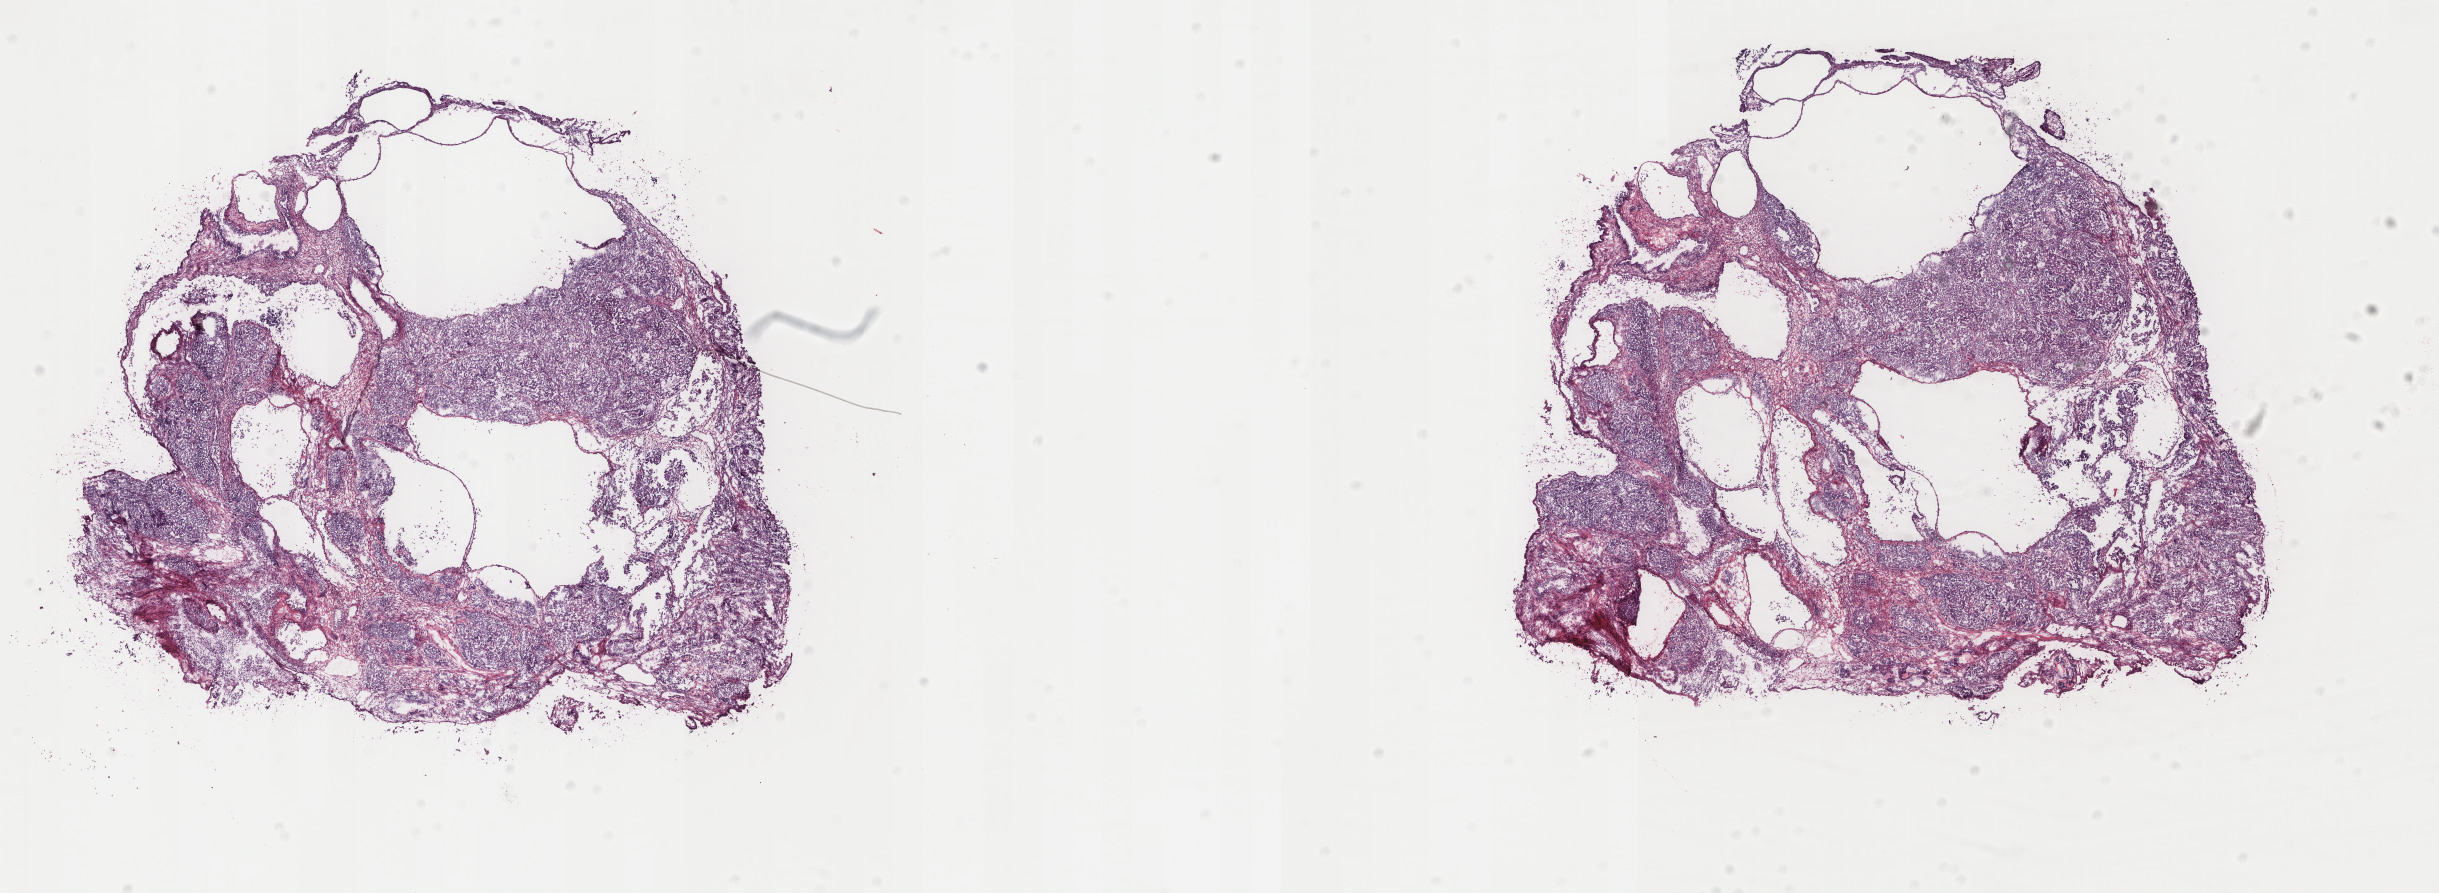
Whole-slide histology image, Hematoxylin and eosin (H&E) stained, low-resolution overview of the scanned area, about 19.4 x 7.1 mm (acquisition: 40x scan). Frozen section from the top of the tissue portion. Sample: primary tumour, uterus. Patient: female, age at initial diagnosis 73 years. Histologic grade: G3 (poorly differentiated). Pathologist review of this section (percent, as recorded): tumour cells 78%, tumour nuclei 90%, normal cells 0%, stromal cells 20%, necrosis 2%. Inflammatory infiltration, as recorded: lymphocyte infiltration 2%, monocyte infiltration 1%, neutrophil infiltration 0%.
FIGO stage: IB. Diagnosis: Endometrioid adenocarcinoma, NOS (endometrium).